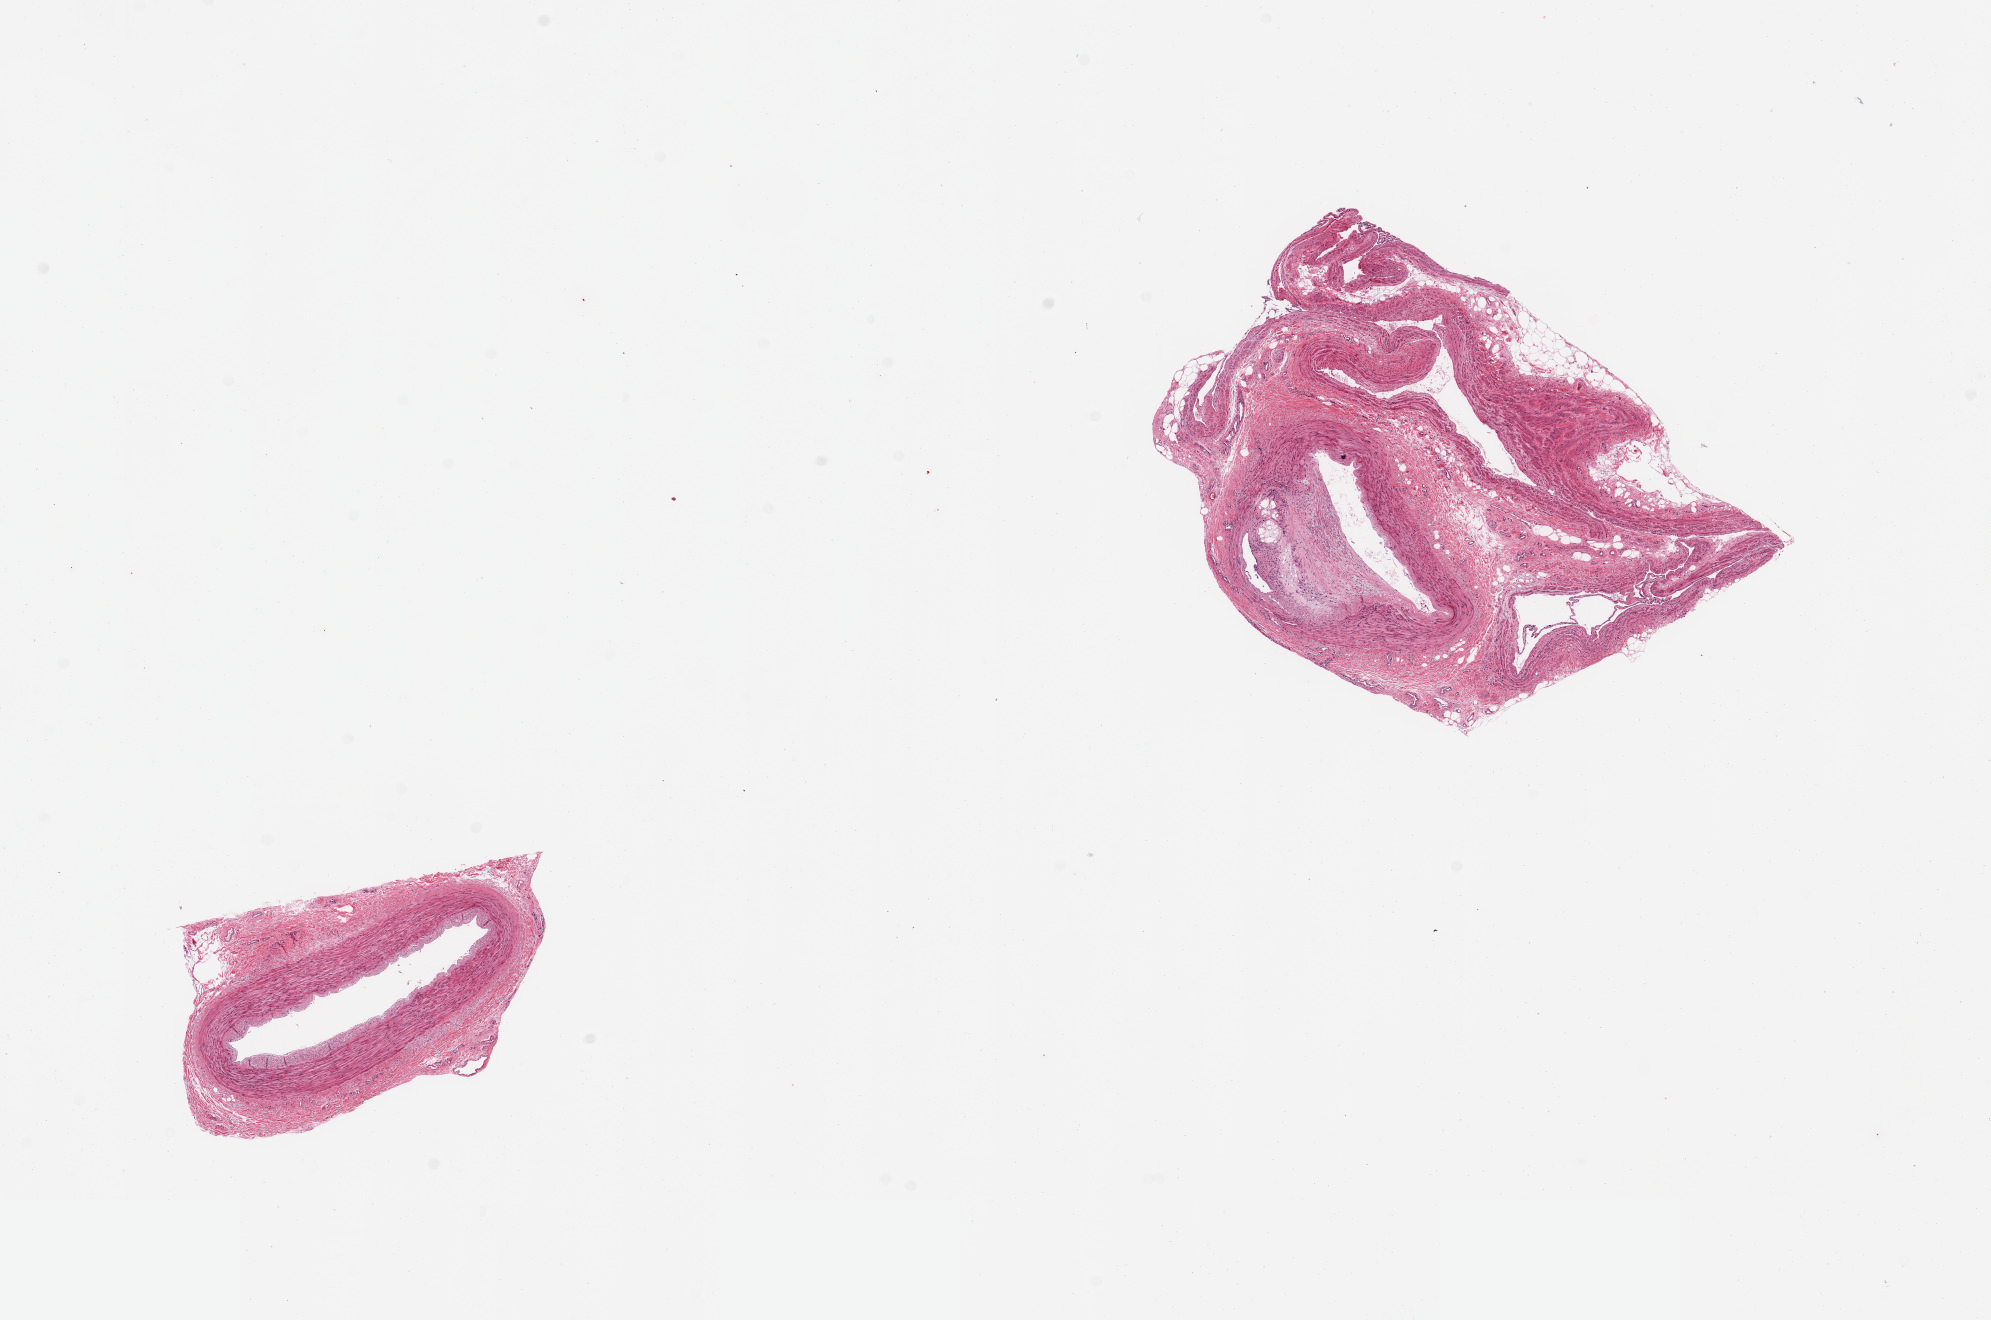
Digitized haematoxylin and eosin-stained section, shown as a low-resolution overview of the whole scanned area (about 15.8 x 10.4 mm, acquisition: 20x scan), PAXgene-fixed paraffin-embedded (PFPE) section, sampled site (target tissue): tibial artery, tissue donor sample.
* reviewer comment on this tissue sample: 2 pieces; one is relatively well trimmed without significant intimal thickening/plaque, second shows significant attachment (60-70%) of vein/fat and artery with 50-75% occlusion by atherosclerosis